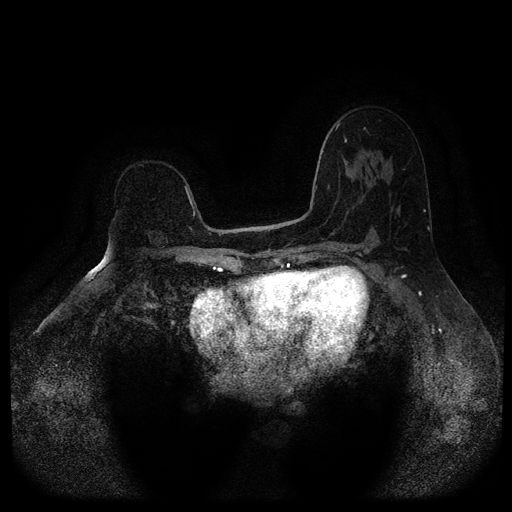
Breast MRI (dynamic contrast-enhanced, multi-phase), one axial slice. Slice 66 of 116 in the series (ordered by position). Dynamic contrast-enhanced series, time point 2 of 5 at this slice position (early post-contrast). 1.5 T. TE 2.6 ms, TR 5.4 ms. 512 × 512 image matrix. Patient: female, 64 years.
Structures marked on this image (semi-automatic segmentation, software-assisted and operator-edited):
- breast lesion (labelled benign in the annotation): bounding box [x1, y1, x2, y2] px = [146, 230, 170, 252]